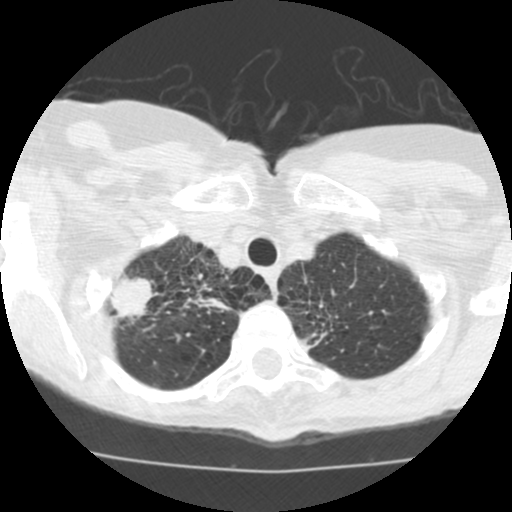
Chest CT (low-dose screening protocol), one axial image; second screening round (one year after baseline); lung window (W 1500 / L -600 HU); 2.5 mm slice thickness; standard (soft-tissue) reconstruction kernel (STANDARD); slice 14 of 115 in the series; 512 × 512 image matrix. Female, age 68 years at enrolment.
Lesion marked by an expert reader, box from (x=100, y=264) to (x=162, y=334) px. The screening reader recorded 3 non-calcified nodules or masses ≥4 mm on this exam (right upper lobe, right upper lobe, right middle lobe); which of them this box marks is not recorded. Official screen result: positive, other. Lung cancer was diagnosed 36 days after this screen: large cell neuroendocrine carcinoma, right upper lobe, undifferentiated (G4), stage IB (AJCC 6th edition), 22 mm at pathology.